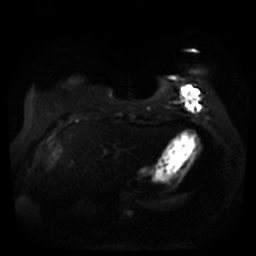
Breast MRI, one axial slice. Slice 8 of 44 in the series (ordered by position). Diffusion-weighted series; image 2 of 4 stored at this slice position (different b-values; order by instance number). 3 T. 5 mm slice thickness. 256 × 256 image matrix, field of view 360 × 360 mm. Female patient.
Annotated regions visible in this slice (manually delineated by an expert):
- tumour on diffusion-weighted imaging: box from (x=182, y=89) to (x=198, y=102) px